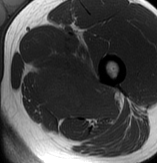
MRI of an extremity soft-tissue mass, one axial slice; position 58 of 70 along the scan axis; MR volume resampled by the dataset authors to the PET/CT grid (not the native acquisition matrix); 3.27 mm slice thickness; 157 × 163 image matrix. Male patient. Case-level facts recorded for this patient, not image findings: histological type: extraskeletal osteosarcoma; grade: high; site of the primary tumour: left adductur.
Structures marked on this image (expert contour drawn on MRI and transferred to this co-registered scan by the dataset authors):
- gross tumour volume (mass): box from (x=31, y=42) to (x=121, y=120) px